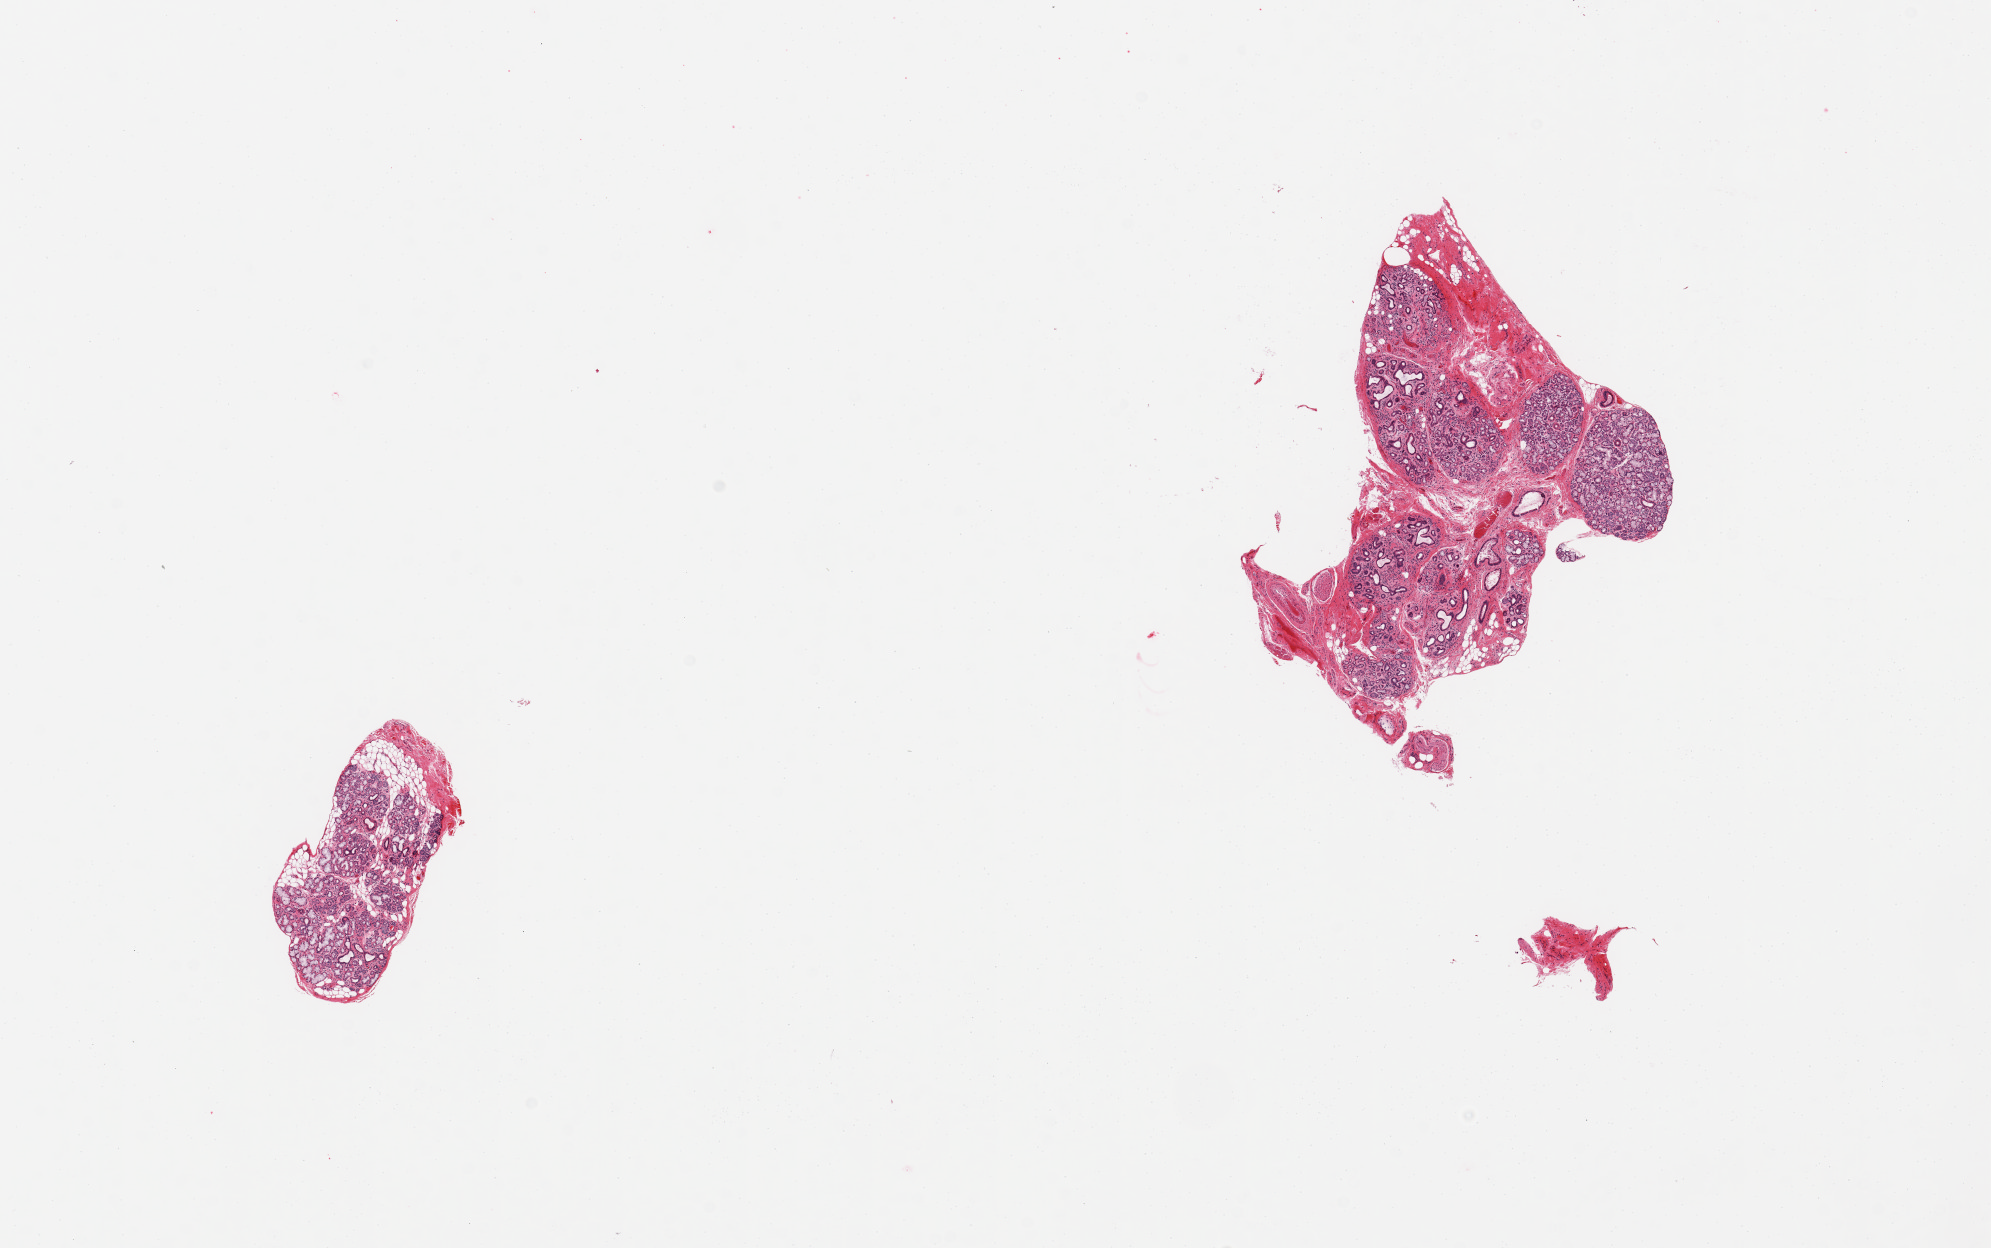
Whole-slide image, haematoxylin and eosin stain — shown as a low-resolution overview of the whole scanned area (about 15.8 x 9.9 mm, acquisition: 20x scan); PAXgene-fixed paraffin-embedded (PFPE) section; sampled site (target tissue): minor salivary gland; tissue donor sample. Donor sex: male.
Review note (as recorded): 2 pieces; good representation of salivary gland elements with some admixed fat and small portion of attached stroma/nerve/vessels, chronic sialadenitis.